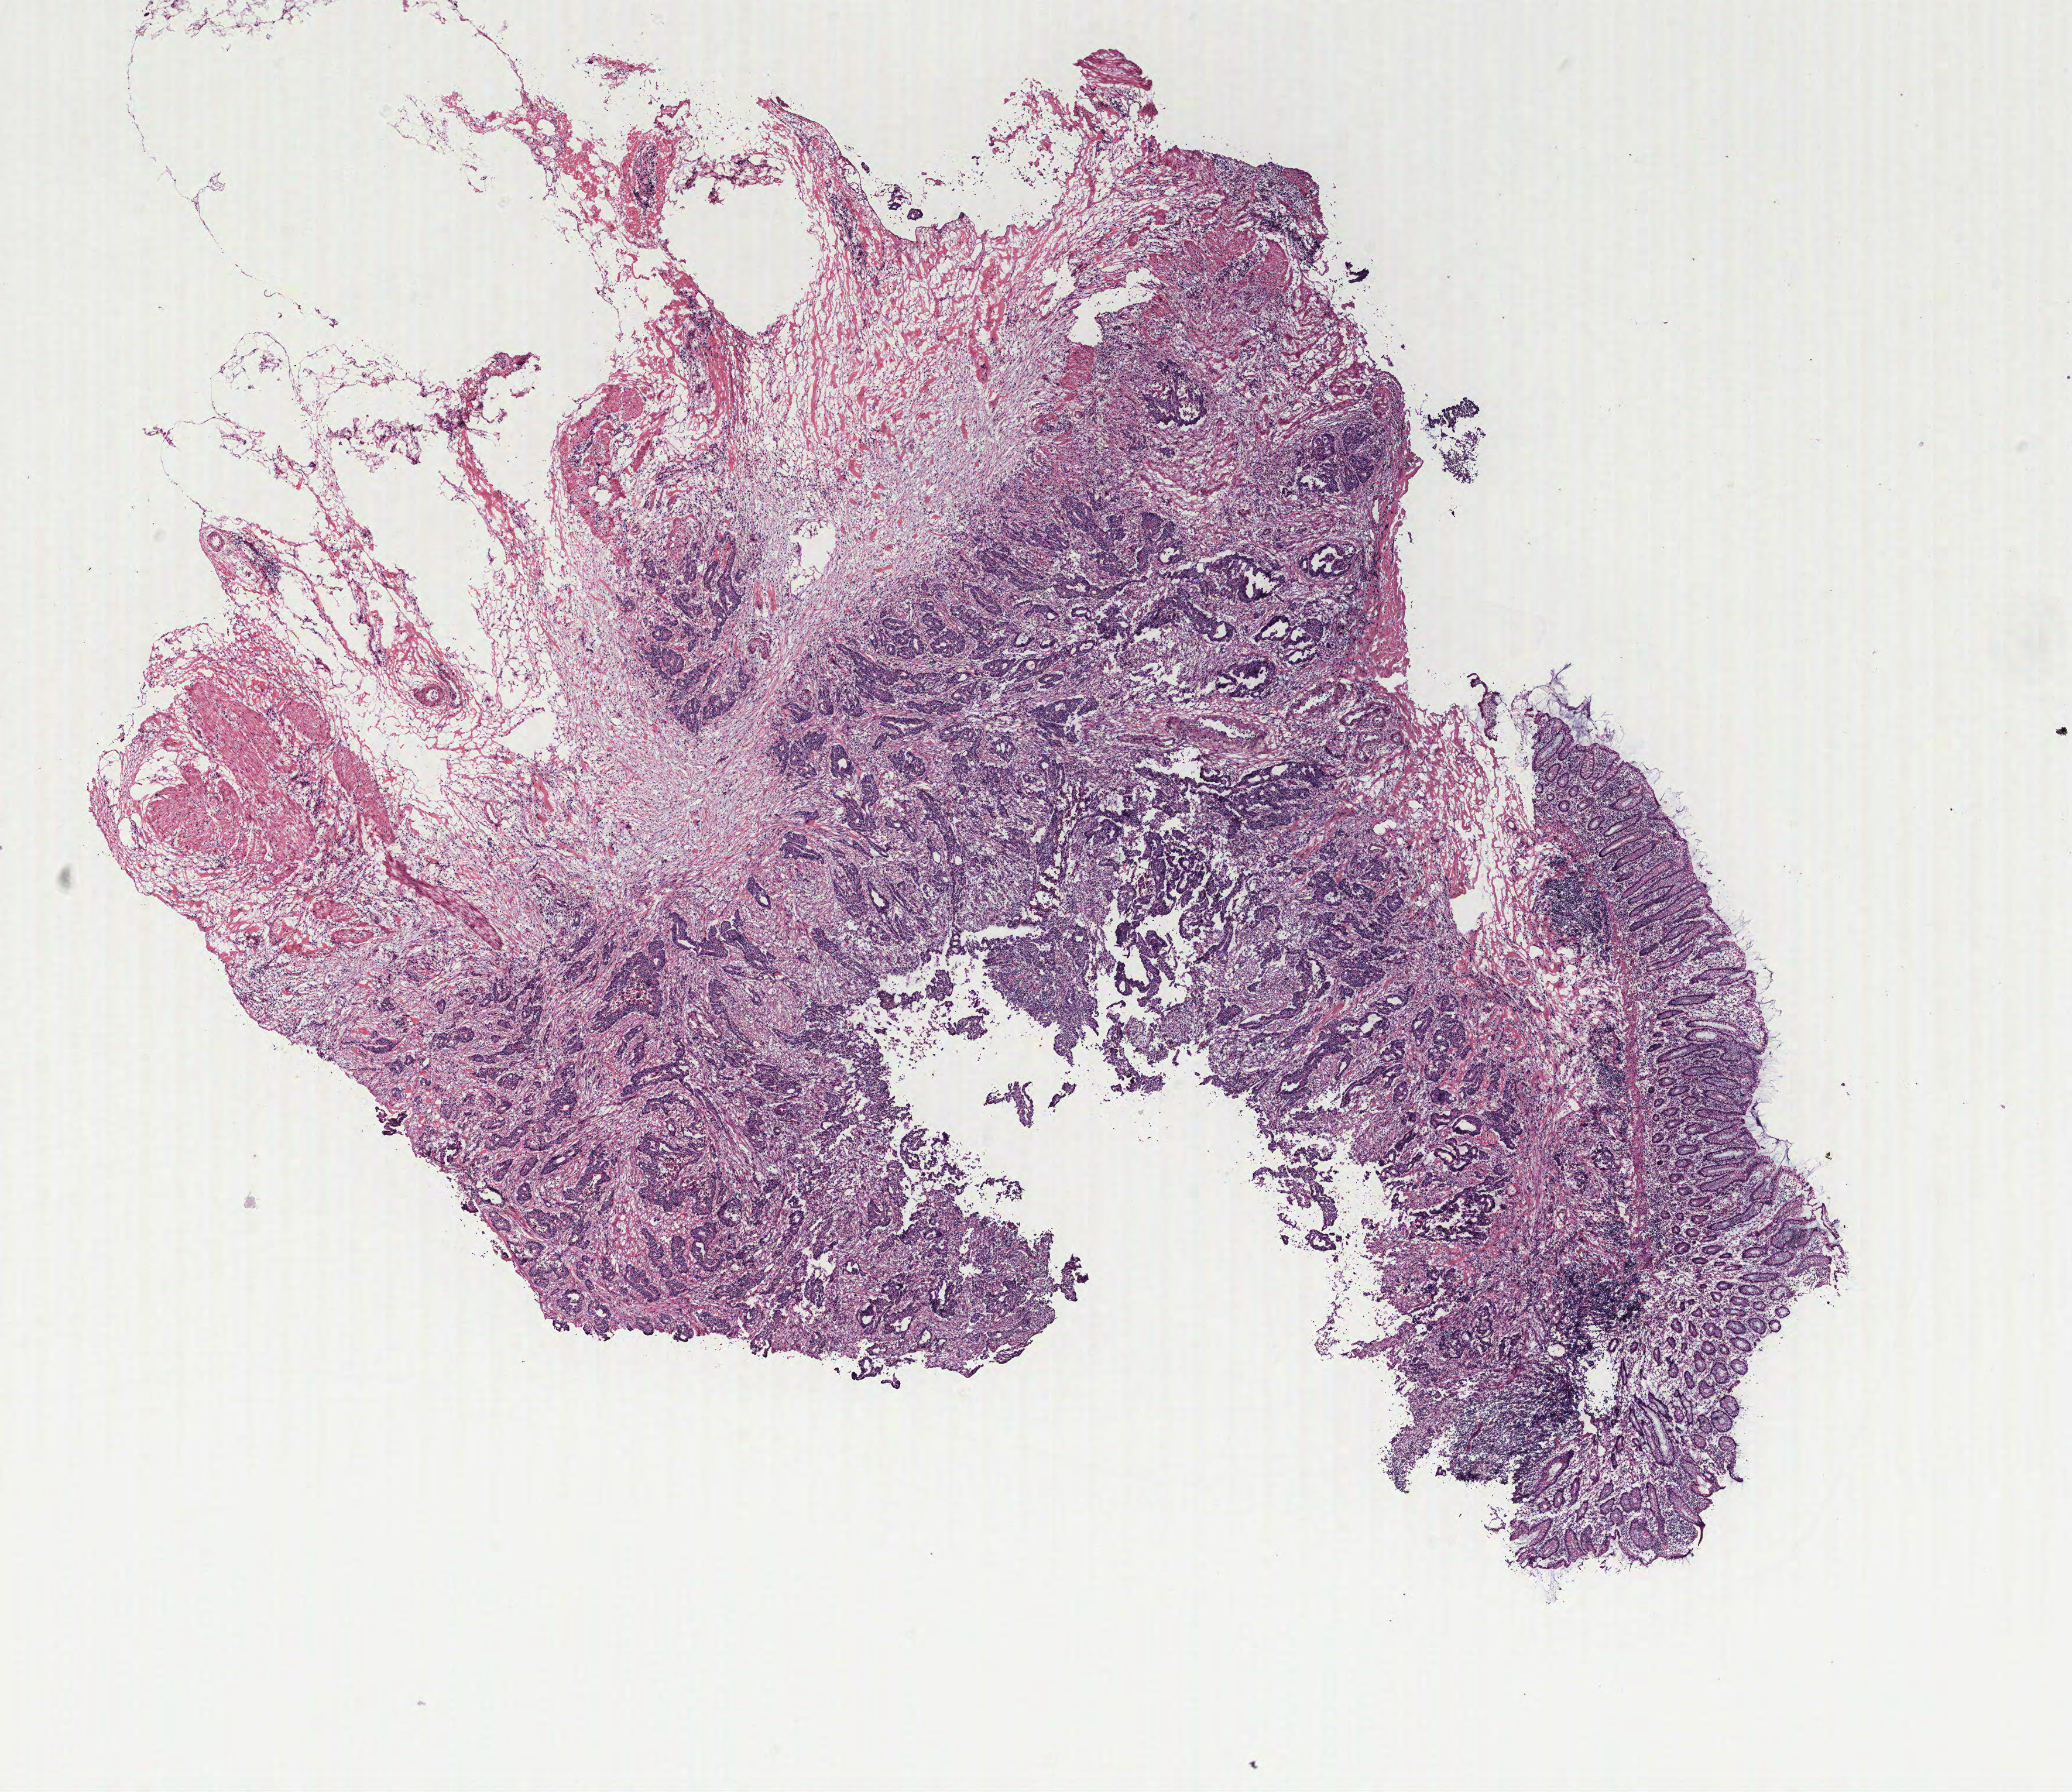
Hematoxylin and eosin (H&E) stained whole-slide image — whole scanned area (about 14.2 x 12.3 mm, slide scanned at 40x) shown as a low-resolution overview; colon, tumour tissue. 50-year-old female patient.
- histologic diagnosis: Adenocarcinoma, NOS
- primary tumour site (as recorded): colon
- AJCC pathologic stage: IIIC